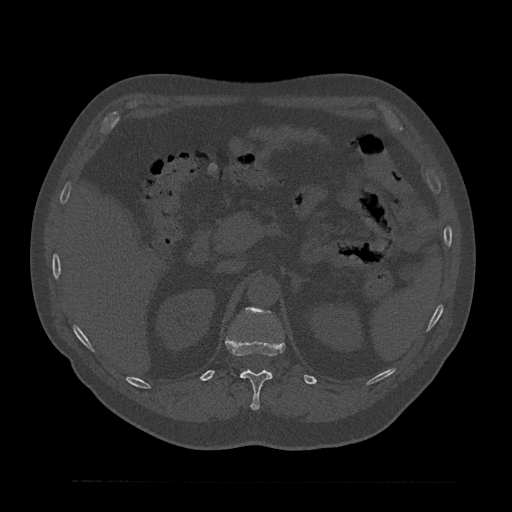
CT including the spine, one axial slice; slice 213 of 797 in the series (ordered by position); bone window (W 1800 / L 400 HU); 0.5 mm slice thickness; 512 × 512 image matrix, field of view 430 × 430 mm. Male patient, age 61 years. Case-level facts recorded for this patient, not image findings: primary cancer: prostate.
Annotated regions visible in this slice (semi-automatic segmentation, software-assisted and operator-edited):
- L1 vertebra: box from (x=247, y=309) to (x=269, y=313) px
- T12 vertebra: (x=225, y=337)–(x=285, y=410)